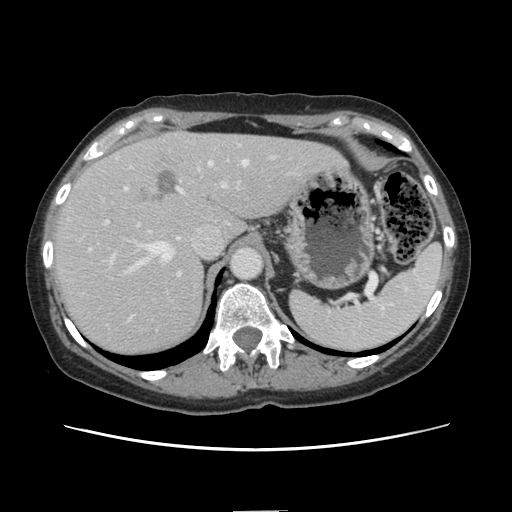
Contrast-enhanced abdominal CT, one axial slice; position 104 of 141 along the scan axis; intravenous contrast given; soft-tissue window (W 400 / L 40 HU); 2.5 mm slice thickness; 512 × 512 image matrix. Female patient, age 63 years. From the clinical record (not read from this slice): diagnosis: colorectal cancer liver metastases, imaged before liver resection; multiple liver metastases: yes; largest metastasis: 3.2 cm.
Structures marked on this image (expert manual segmentation):
- hepatic veins: bounding box (x1, y1, x2, y2) in pixels: (126, 160, 248, 273)
- liver: (53, 132, 341, 356)
- planned liver remnant (the part of the liver to remain after resection): (186, 133, 342, 239)
- portal vein (with intrahepatic branches): (105, 183, 227, 275)